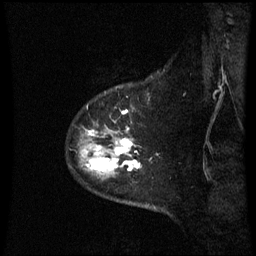
Breast MRI (dynamic contrast-enhanced), one sagittal slice; dynamic contrast-enhanced series, image 2 of 3 at this slice position (ordered by acquisition); 1.5 T; TE 4.2 ms, TR 8.9 ms; 2.3 mm slice thickness; 256 × 256 image matrix, field of view 210 × 210 mm. Patient: female, 43 years. From the clinical record (not read from this slice): setting: breast cancer imaged before/during neoadjuvant chemotherapy; receptor status: HER2-positive.
Outlined on this slice (semi-automatic segmentation, software-assisted and operator-edited):
- analysis volume of interest (the breast-tissue region the enhancement analysis was run in; not a lesion): bounding box (x1, y1, x2, y2) in pixels: (79, 87, 159, 181)
- tumour enhancement mask (voxels above the 70 % enhancement threshold inside the analysis volume of interest): (88, 111, 141, 173)